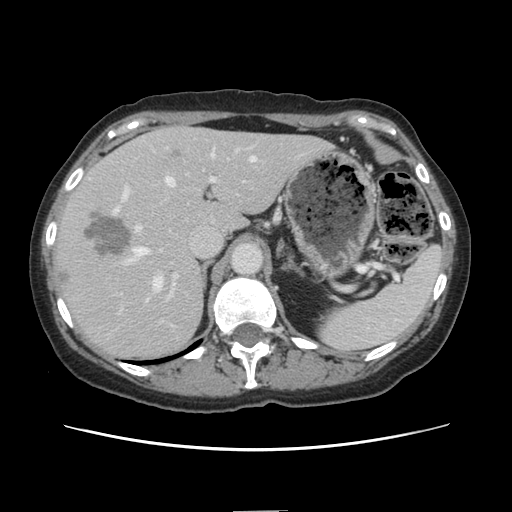
Contrast-enhanced abdominal CT, one axial slice. Slice 96 of 141 in the series (ordered by position). 120 kVp. Intravenous contrast given. Soft-tissue window (W 400 / L 40 HU). 2.5 mm slice thickness. 512 × 512 image matrix, field of view 350 × 350 mm. Female patient, age 63 years. From the clinical record (not read from this slice): diagnosis: colorectal cancer liver metastases, imaged before liver resection; multiple liver metastases: yes; largest metastasis: 3.2 cm; disease in both lobes: yes.
Outlined on this slice (expert manual segmentation):
- hepatic veins: bounding box <129,152,255,289> (left, top, right, bottom; pixels)
- liver: <53,128,330,361>
- planned liver remnant (the part of the liver to remain after resection): <183,129,329,236>
- portal vein (with intrahepatic branches): <113,149,253,302>